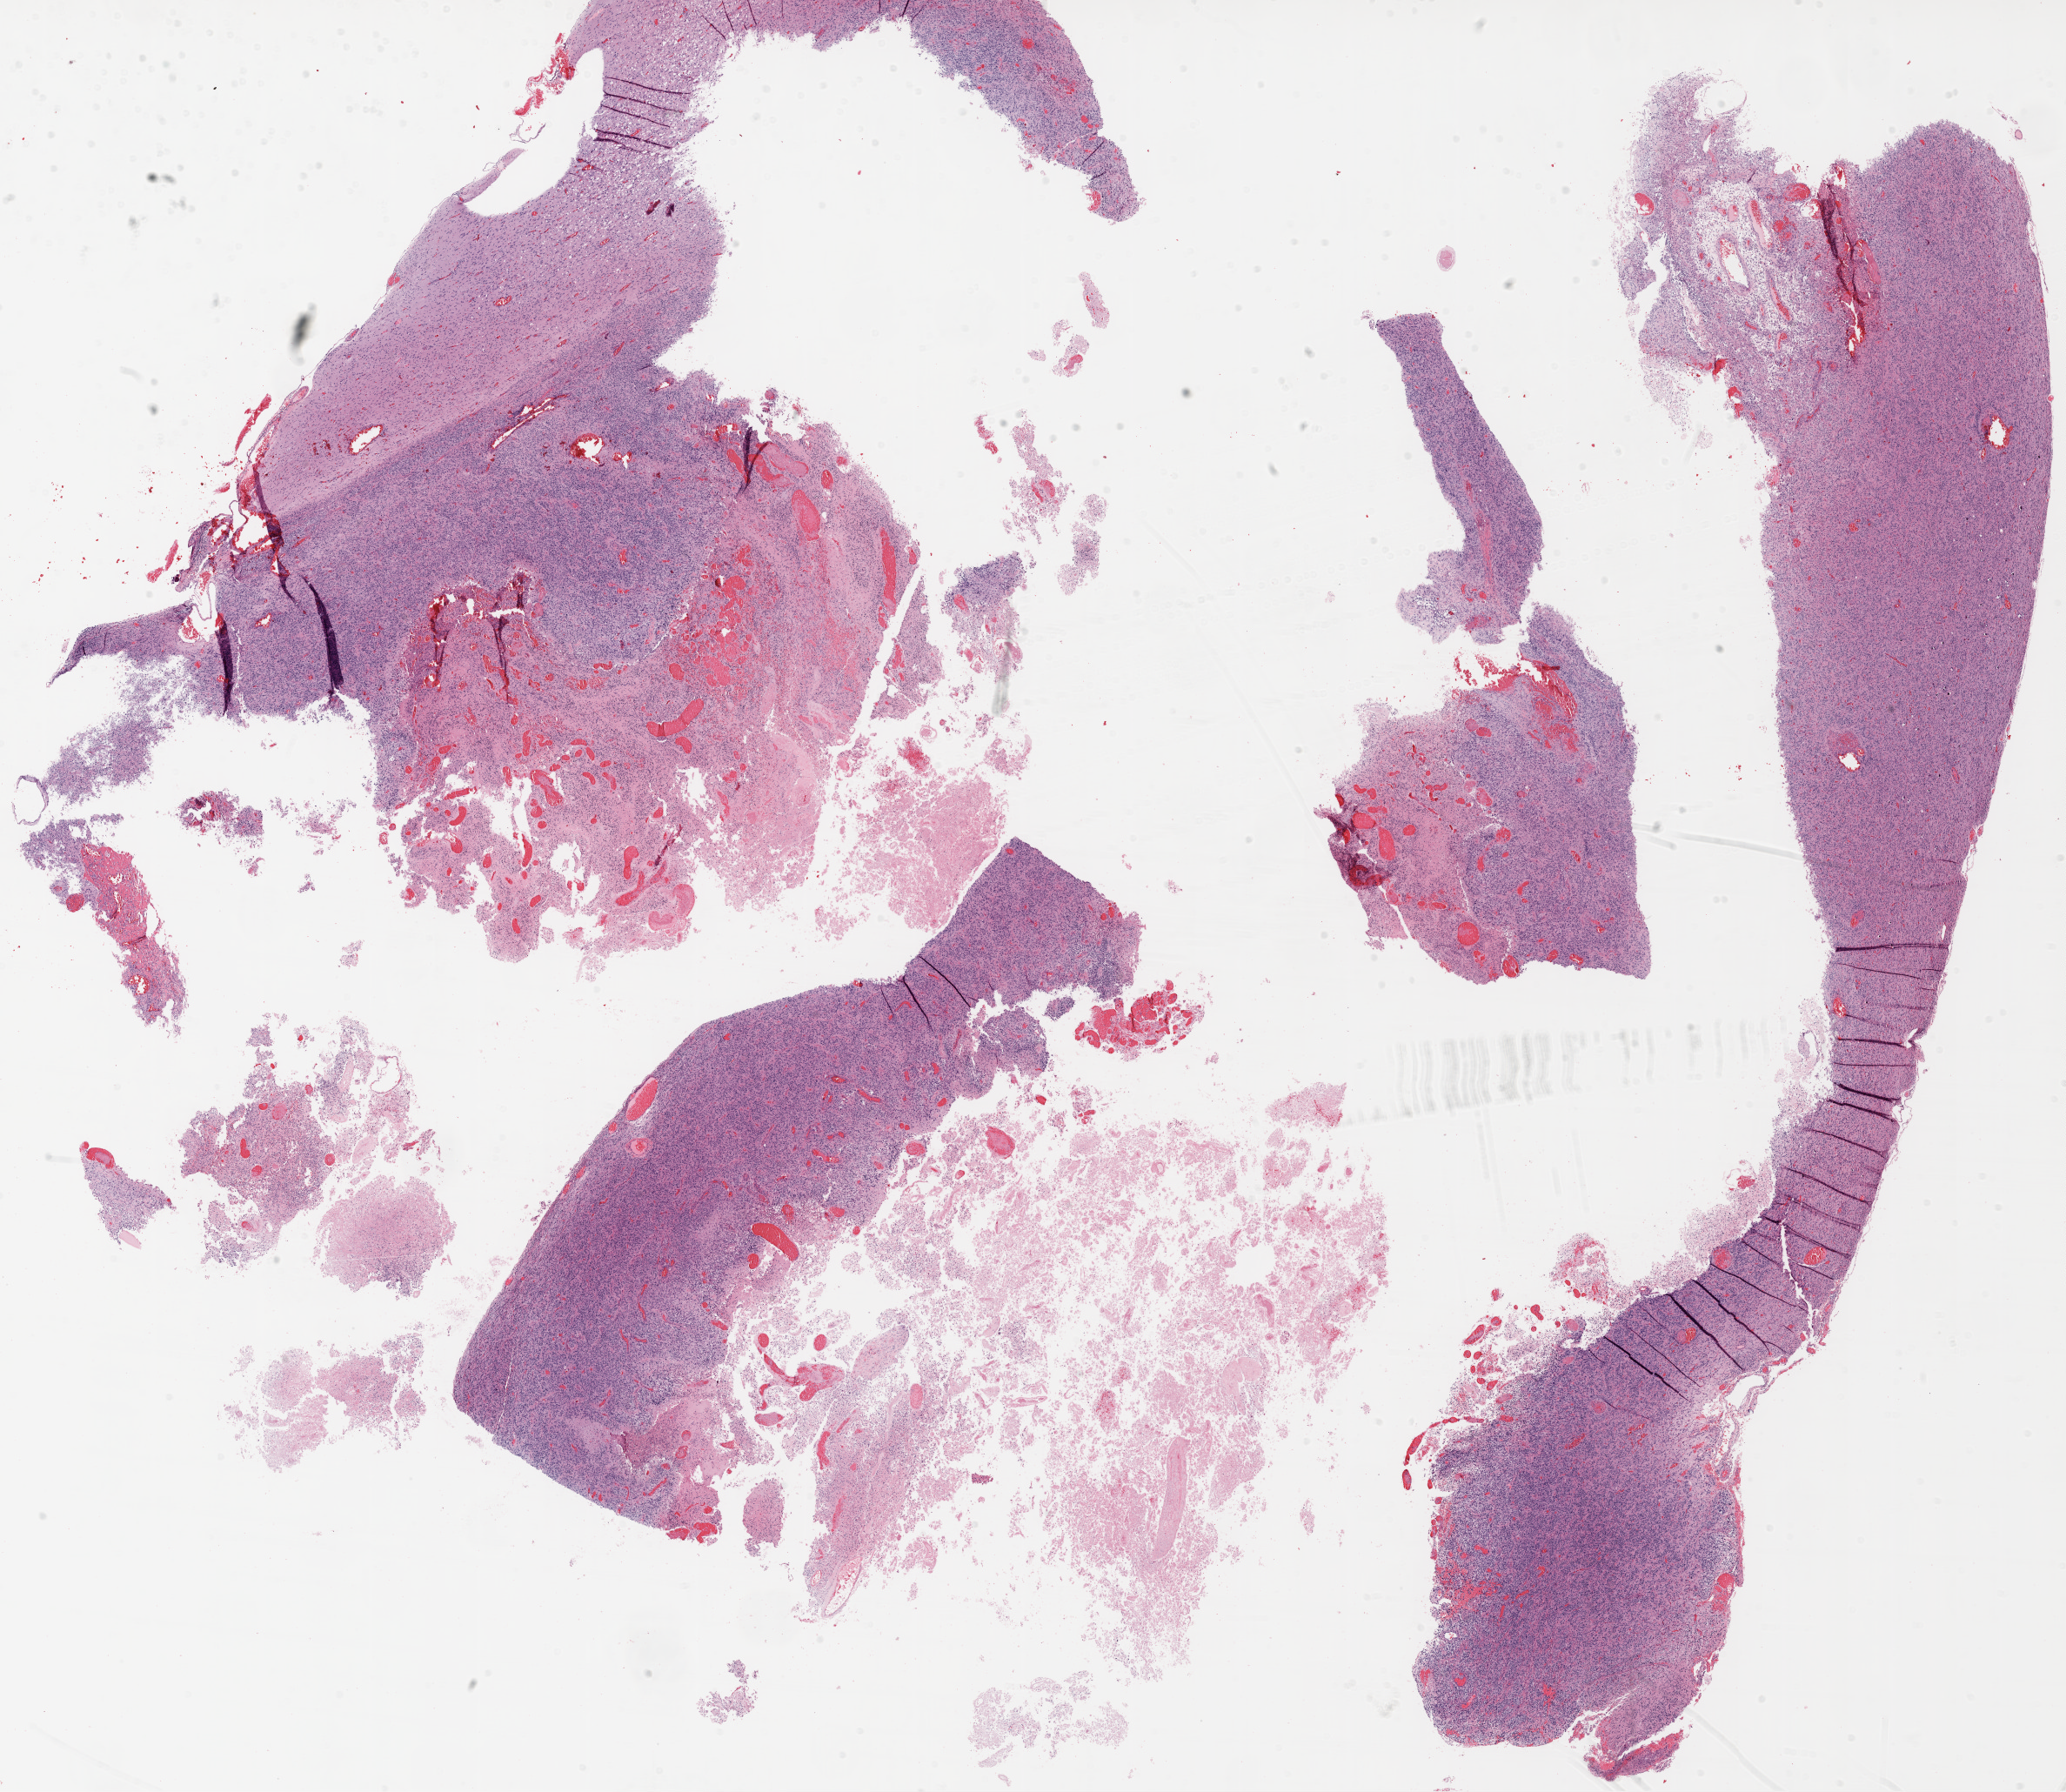
Whole-slide histology image, Hematoxylin and eosin (H&E) stained — shown as a low-resolution overview of the whole scanned area (about 19.1 x 16.5 mm, slide scanned at 20x); FFPE section; brain, primary tumour sample. Patient: male, age at initial diagnosis 39 years.
Histologic diagnosis: Glioblastoma.